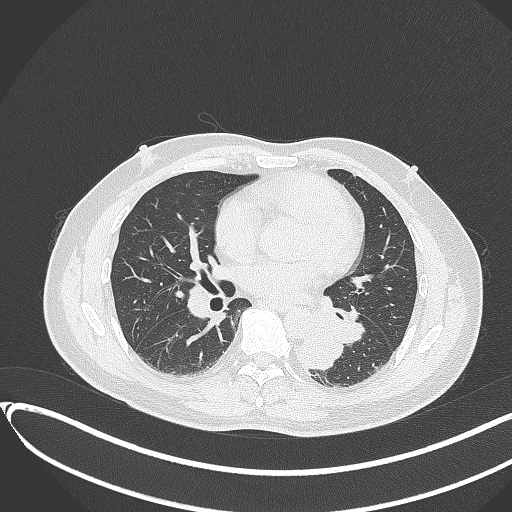
Chest CT, one axial slice; position 161 of 417 along the scan axis; reconstruction kernel B70f; 120 kVp; lung window (W 1500 / L -600 HU); 1 mm slice thickness; 512 × 512 image matrix. Male patient, age 54 years. From the clinical record (not read from this slice): clinical TNM (as recorded): T3 N0 M0.
Outlined on this slice (rectangle marked by the reading radiologist):
- lung tumour (recorded histology: squamous cell carcinoma): bounding box <295,325,345,373> (left, top, right, bottom; pixels)